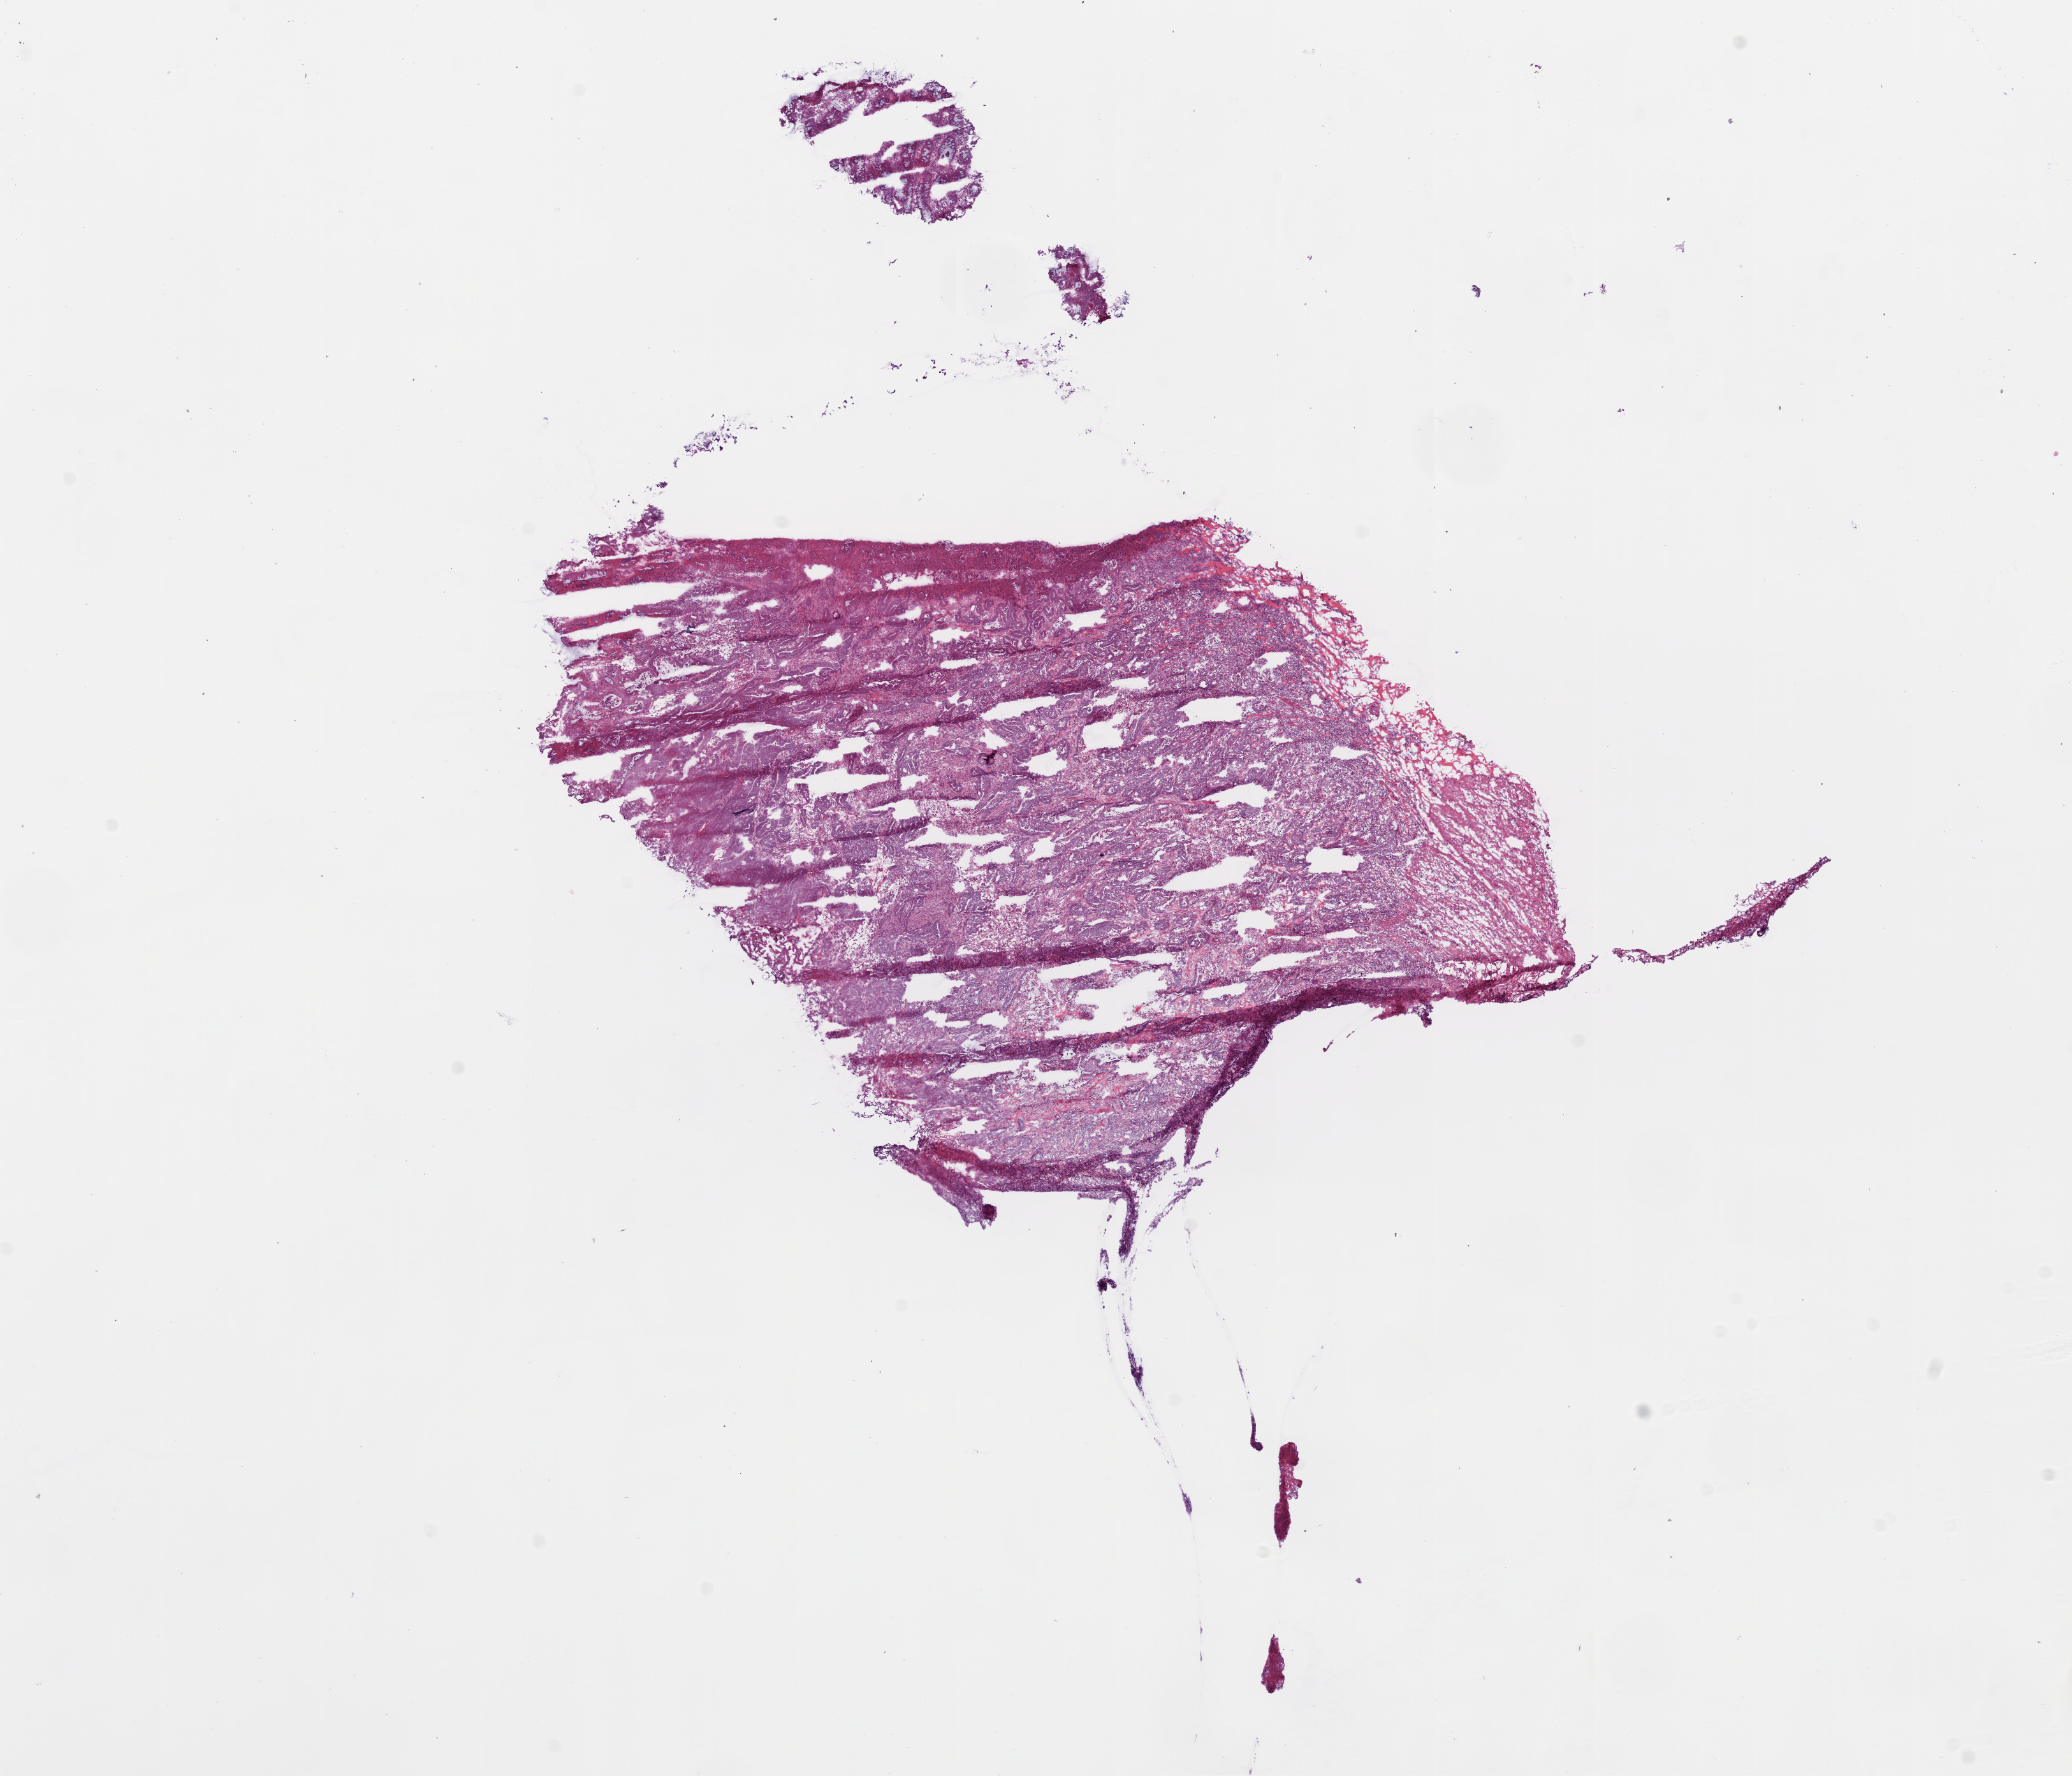
Digitized H&E-stained tissue section (whole slide) — whole scanned area (about 13.0 x 11.2 mm) shown as a low-resolution overview, frozen section, primary tumour sample from the colon. Patient: female, age at initial diagnosis 63 years. Composition of this section per pathologist review: tumour cells 80%, tumour nuclei 85%, normal cells 0%, stromal cells 10%, necrosis 10%.
- pathologic diagnosis: Adenocarcinoma, NOS
- AJCC pathologic stage: IIA